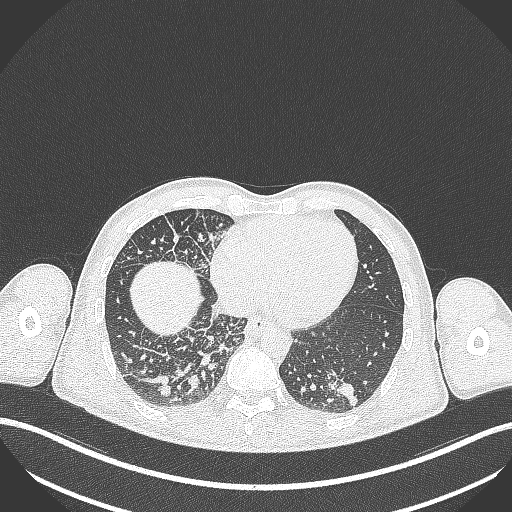
Chest CT, one axial slice. Slice 92 of 348 in the series (ordered by position). 120 kVp. Lung window (W 1500 / L -600 HU). 1 mm slice thickness. 512 × 512 image matrix, field of view 400 × 400 mm. Patient: male, 49 years. Case-level facts recorded for this patient, not image findings: clinical TNM (as recorded): T2b N1 M0.
Structures marked on this image (bounding box drawn by a radiologist):
- lung tumour (recorded histology: adenocarcinoma): bounding box <323,365,359,406> (left, top, right, bottom; pixels)